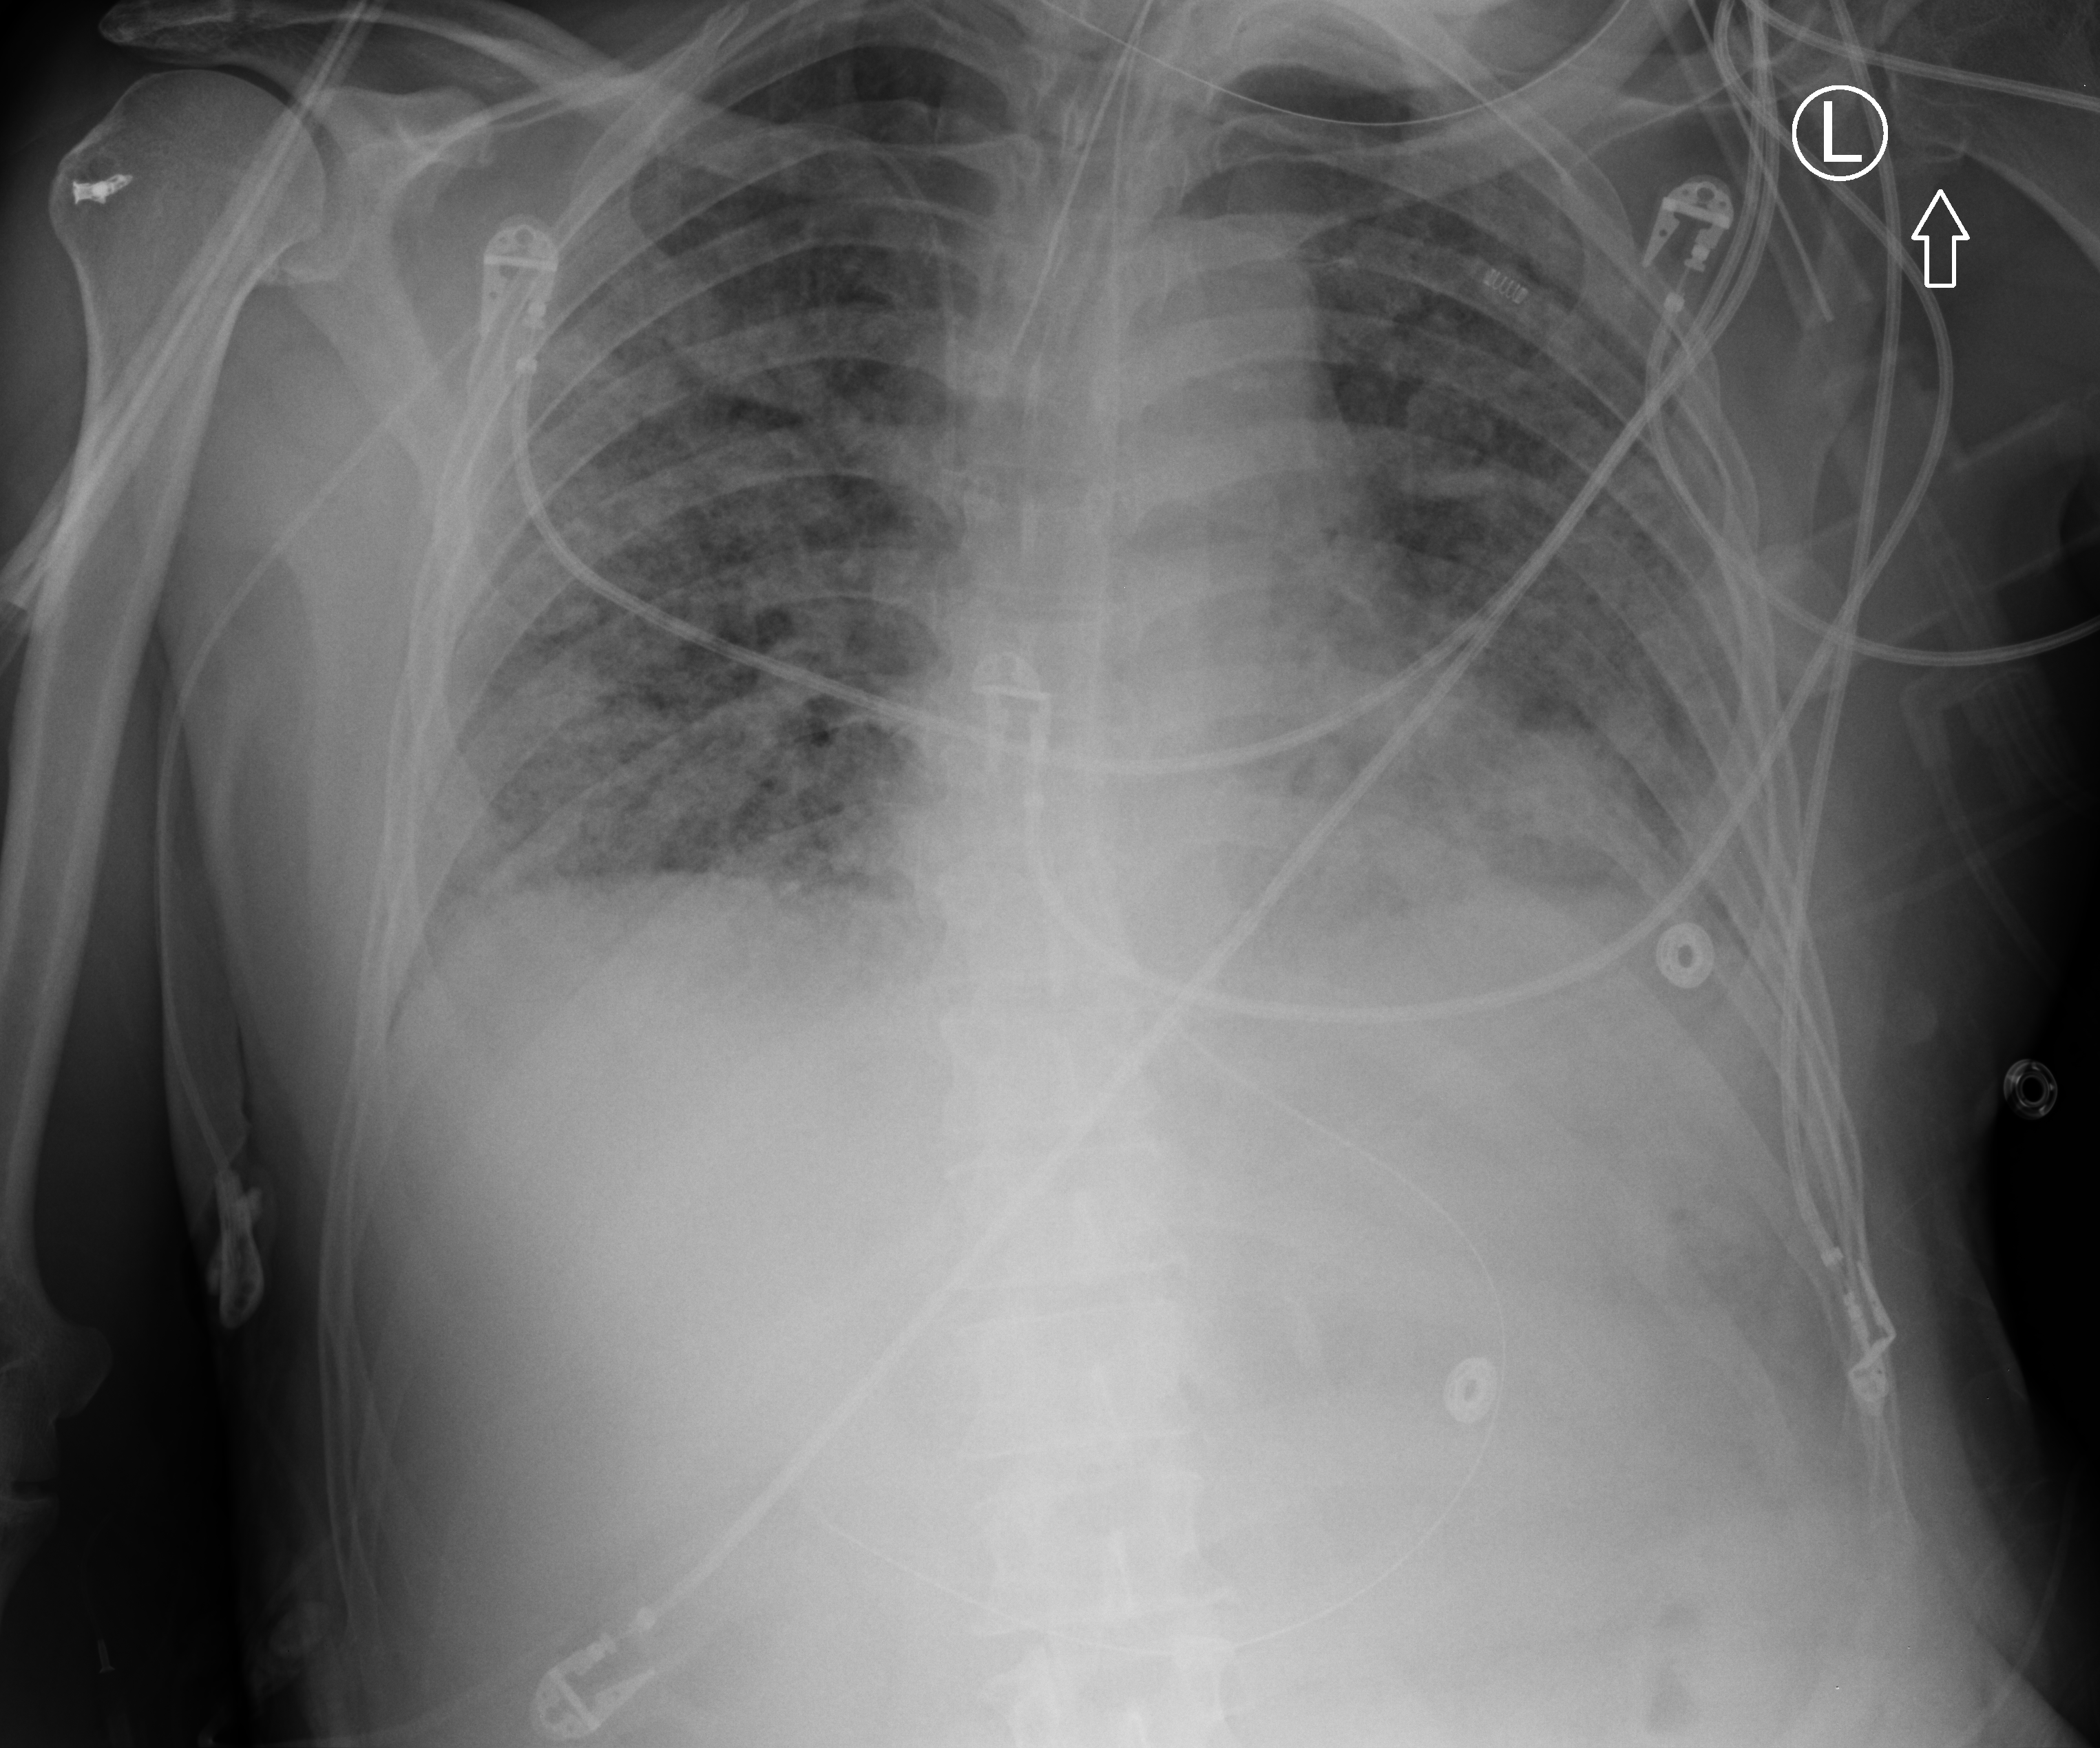
Chest X-ray (portable), anteroposterior (AP) projection. Patient hospitalised with COVID-19; male, aged 60–74 years.
From the hospital-stay record, not from the radiograph (when in the stay this image was taken is not recorded):
- other chronic lung disease (admission record): yes
- hypertension (admission record): no
- smoking status (admission record): never